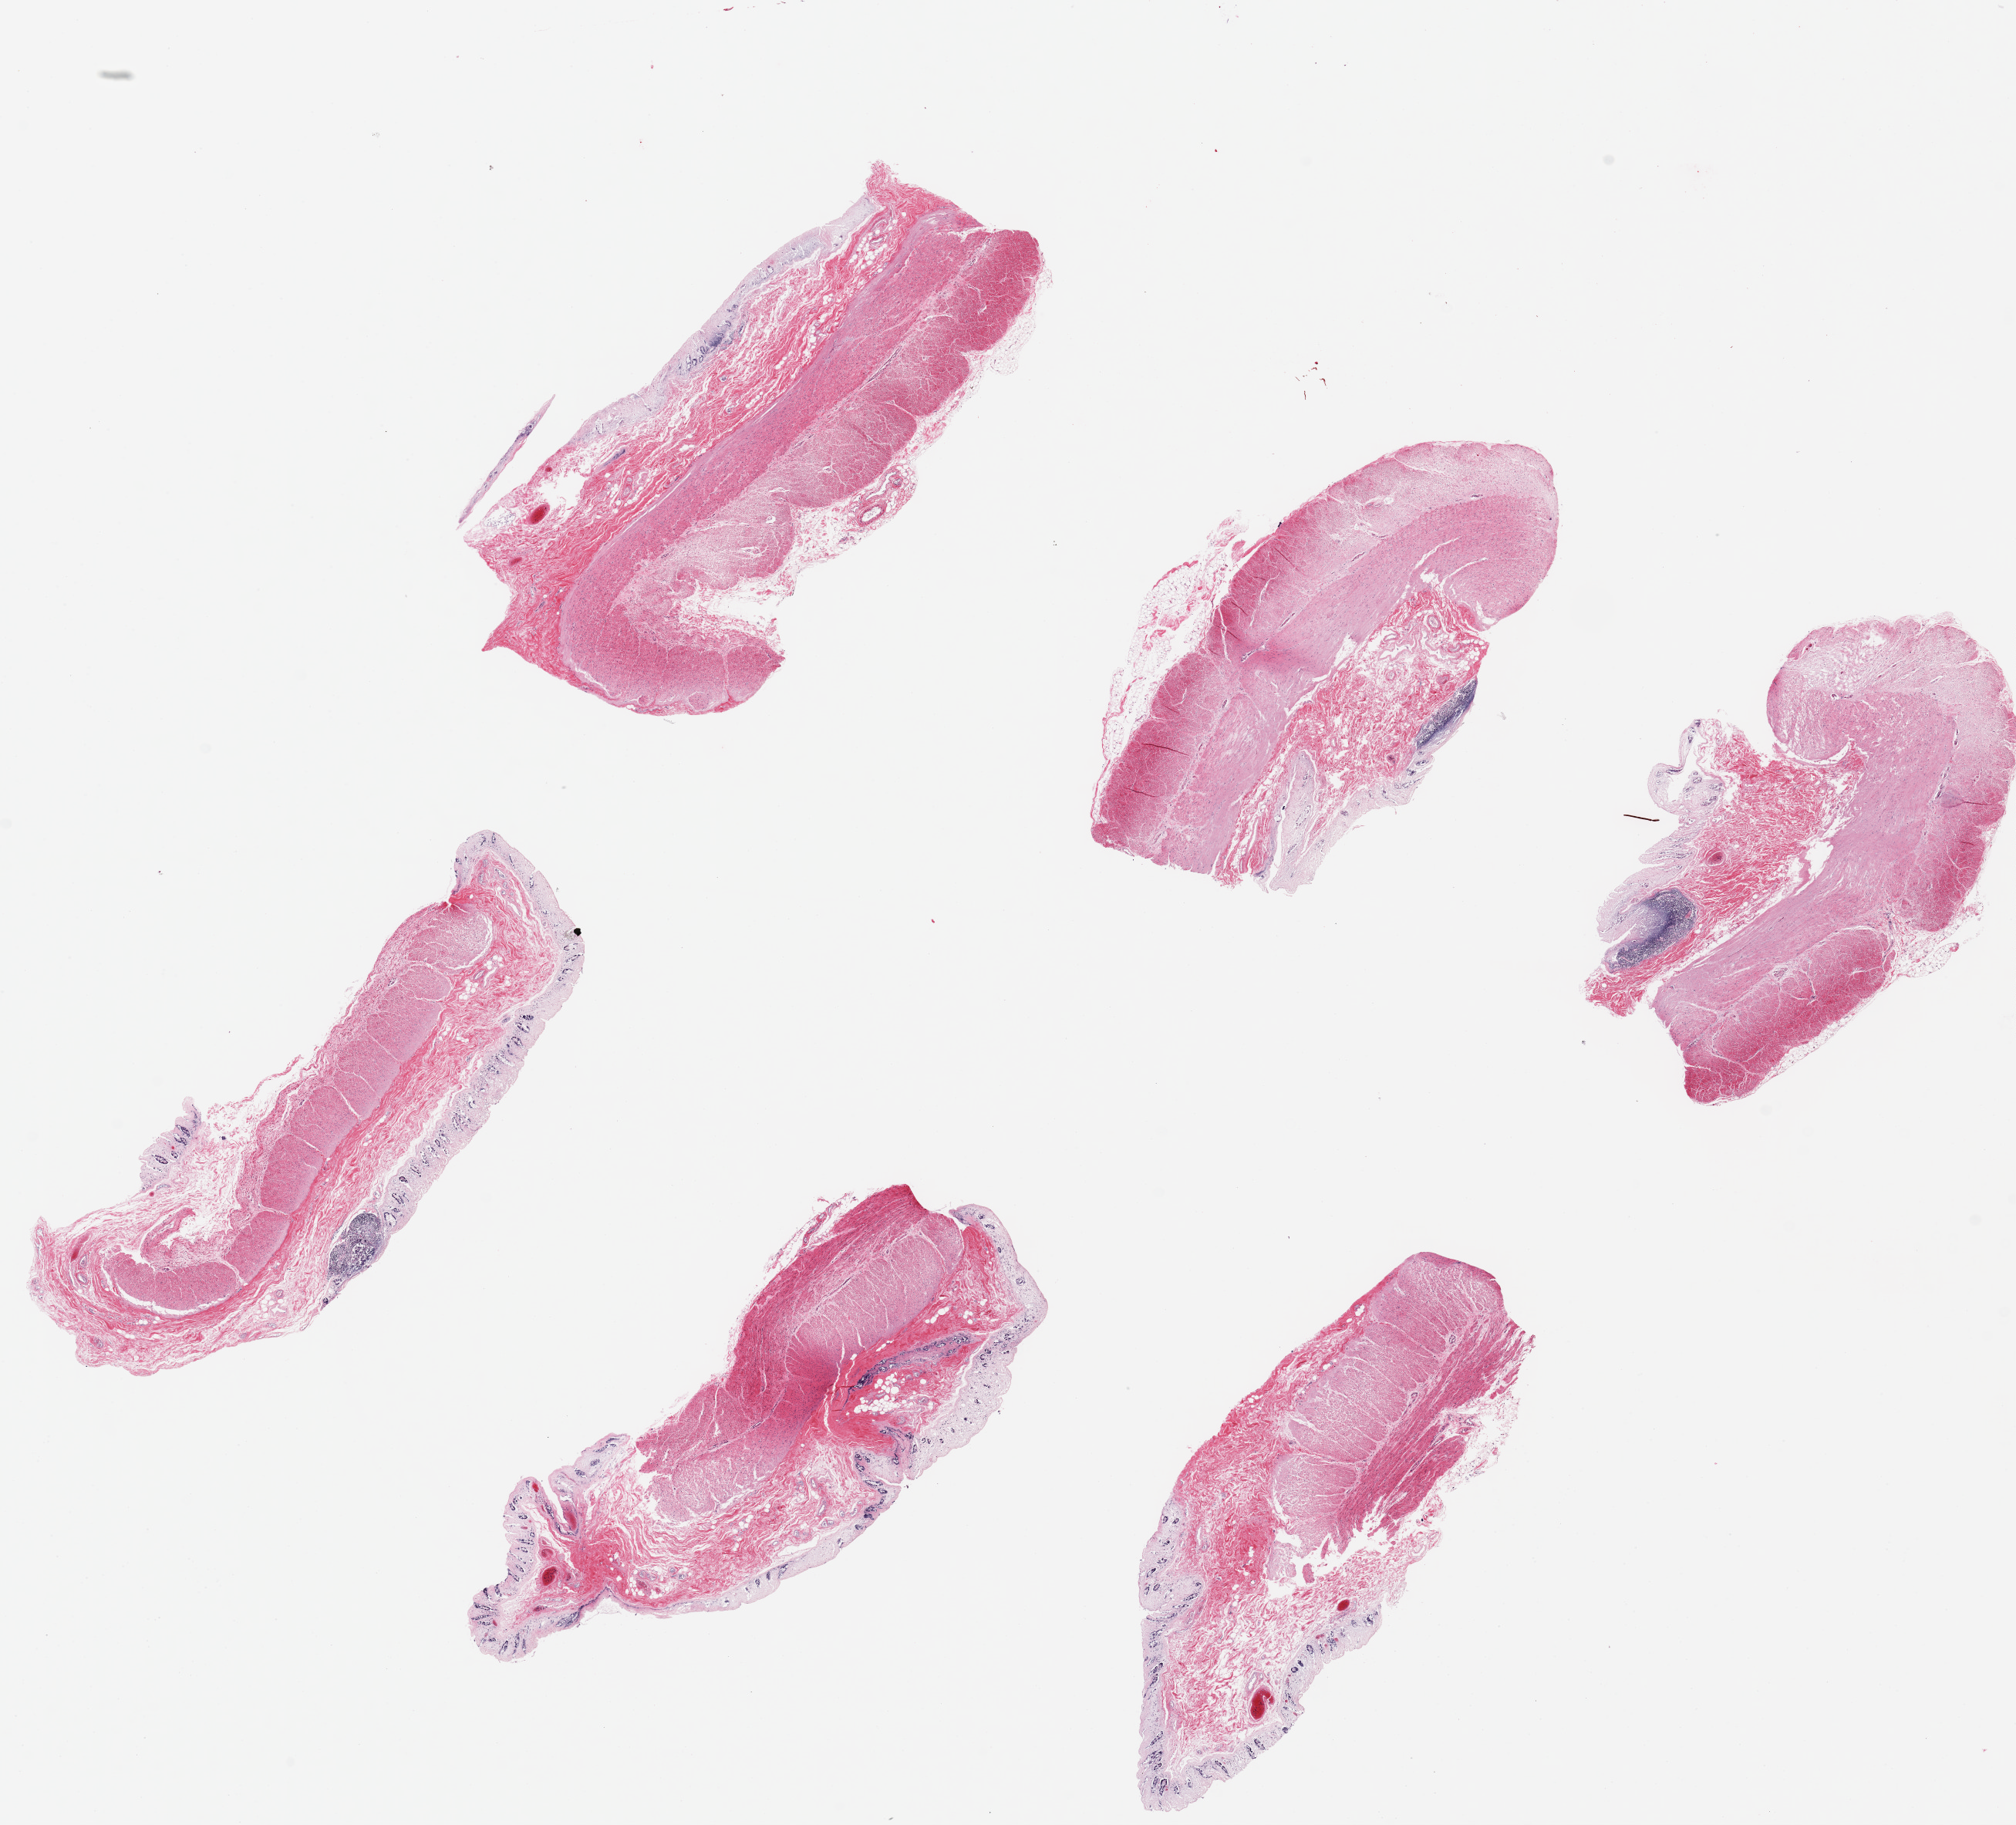
Whole-slide image, haematoxylin and eosin stain, shown as a low-resolution overview of the whole scanned area (about 20.7 x 18.7 mm). PAXgene-fixed, paraffin-embedded tissue. Target tissue: transverse colon. Tissue donor sample. Donor sex: male.
Review note (as recorded): 6 pieces ~6x2.5mm. Mucosa sloughed or badly autolyzed.